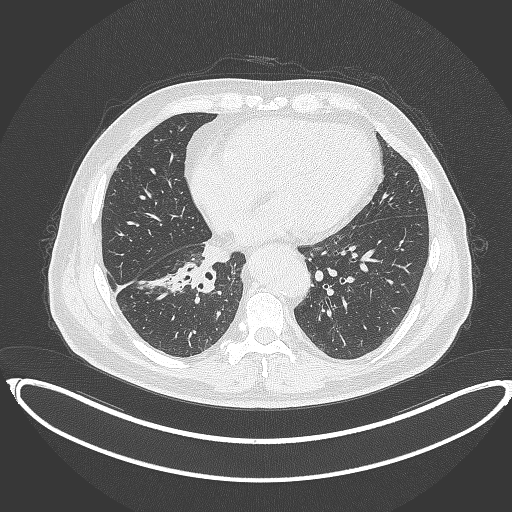
Chest CT, one axial slice; position 156 of 387 along the scan axis; reconstruction kernel B70f; 120 kVp; lung window (W 1500 / L -600 HU); 512 × 512 image matrix, field of view 448 × 448 mm. Male patient, age 61 years. Case-level facts recorded for this patient, not image findings: clinical TNM (as recorded): T1b N1 M0.
Annotated regions visible in this slice (bounding box drawn by a radiologist):
- lung tumour (recorded histology: squamous cell carcinoma): bounding box <171,255,217,298> (left, top, right, bottom; pixels)